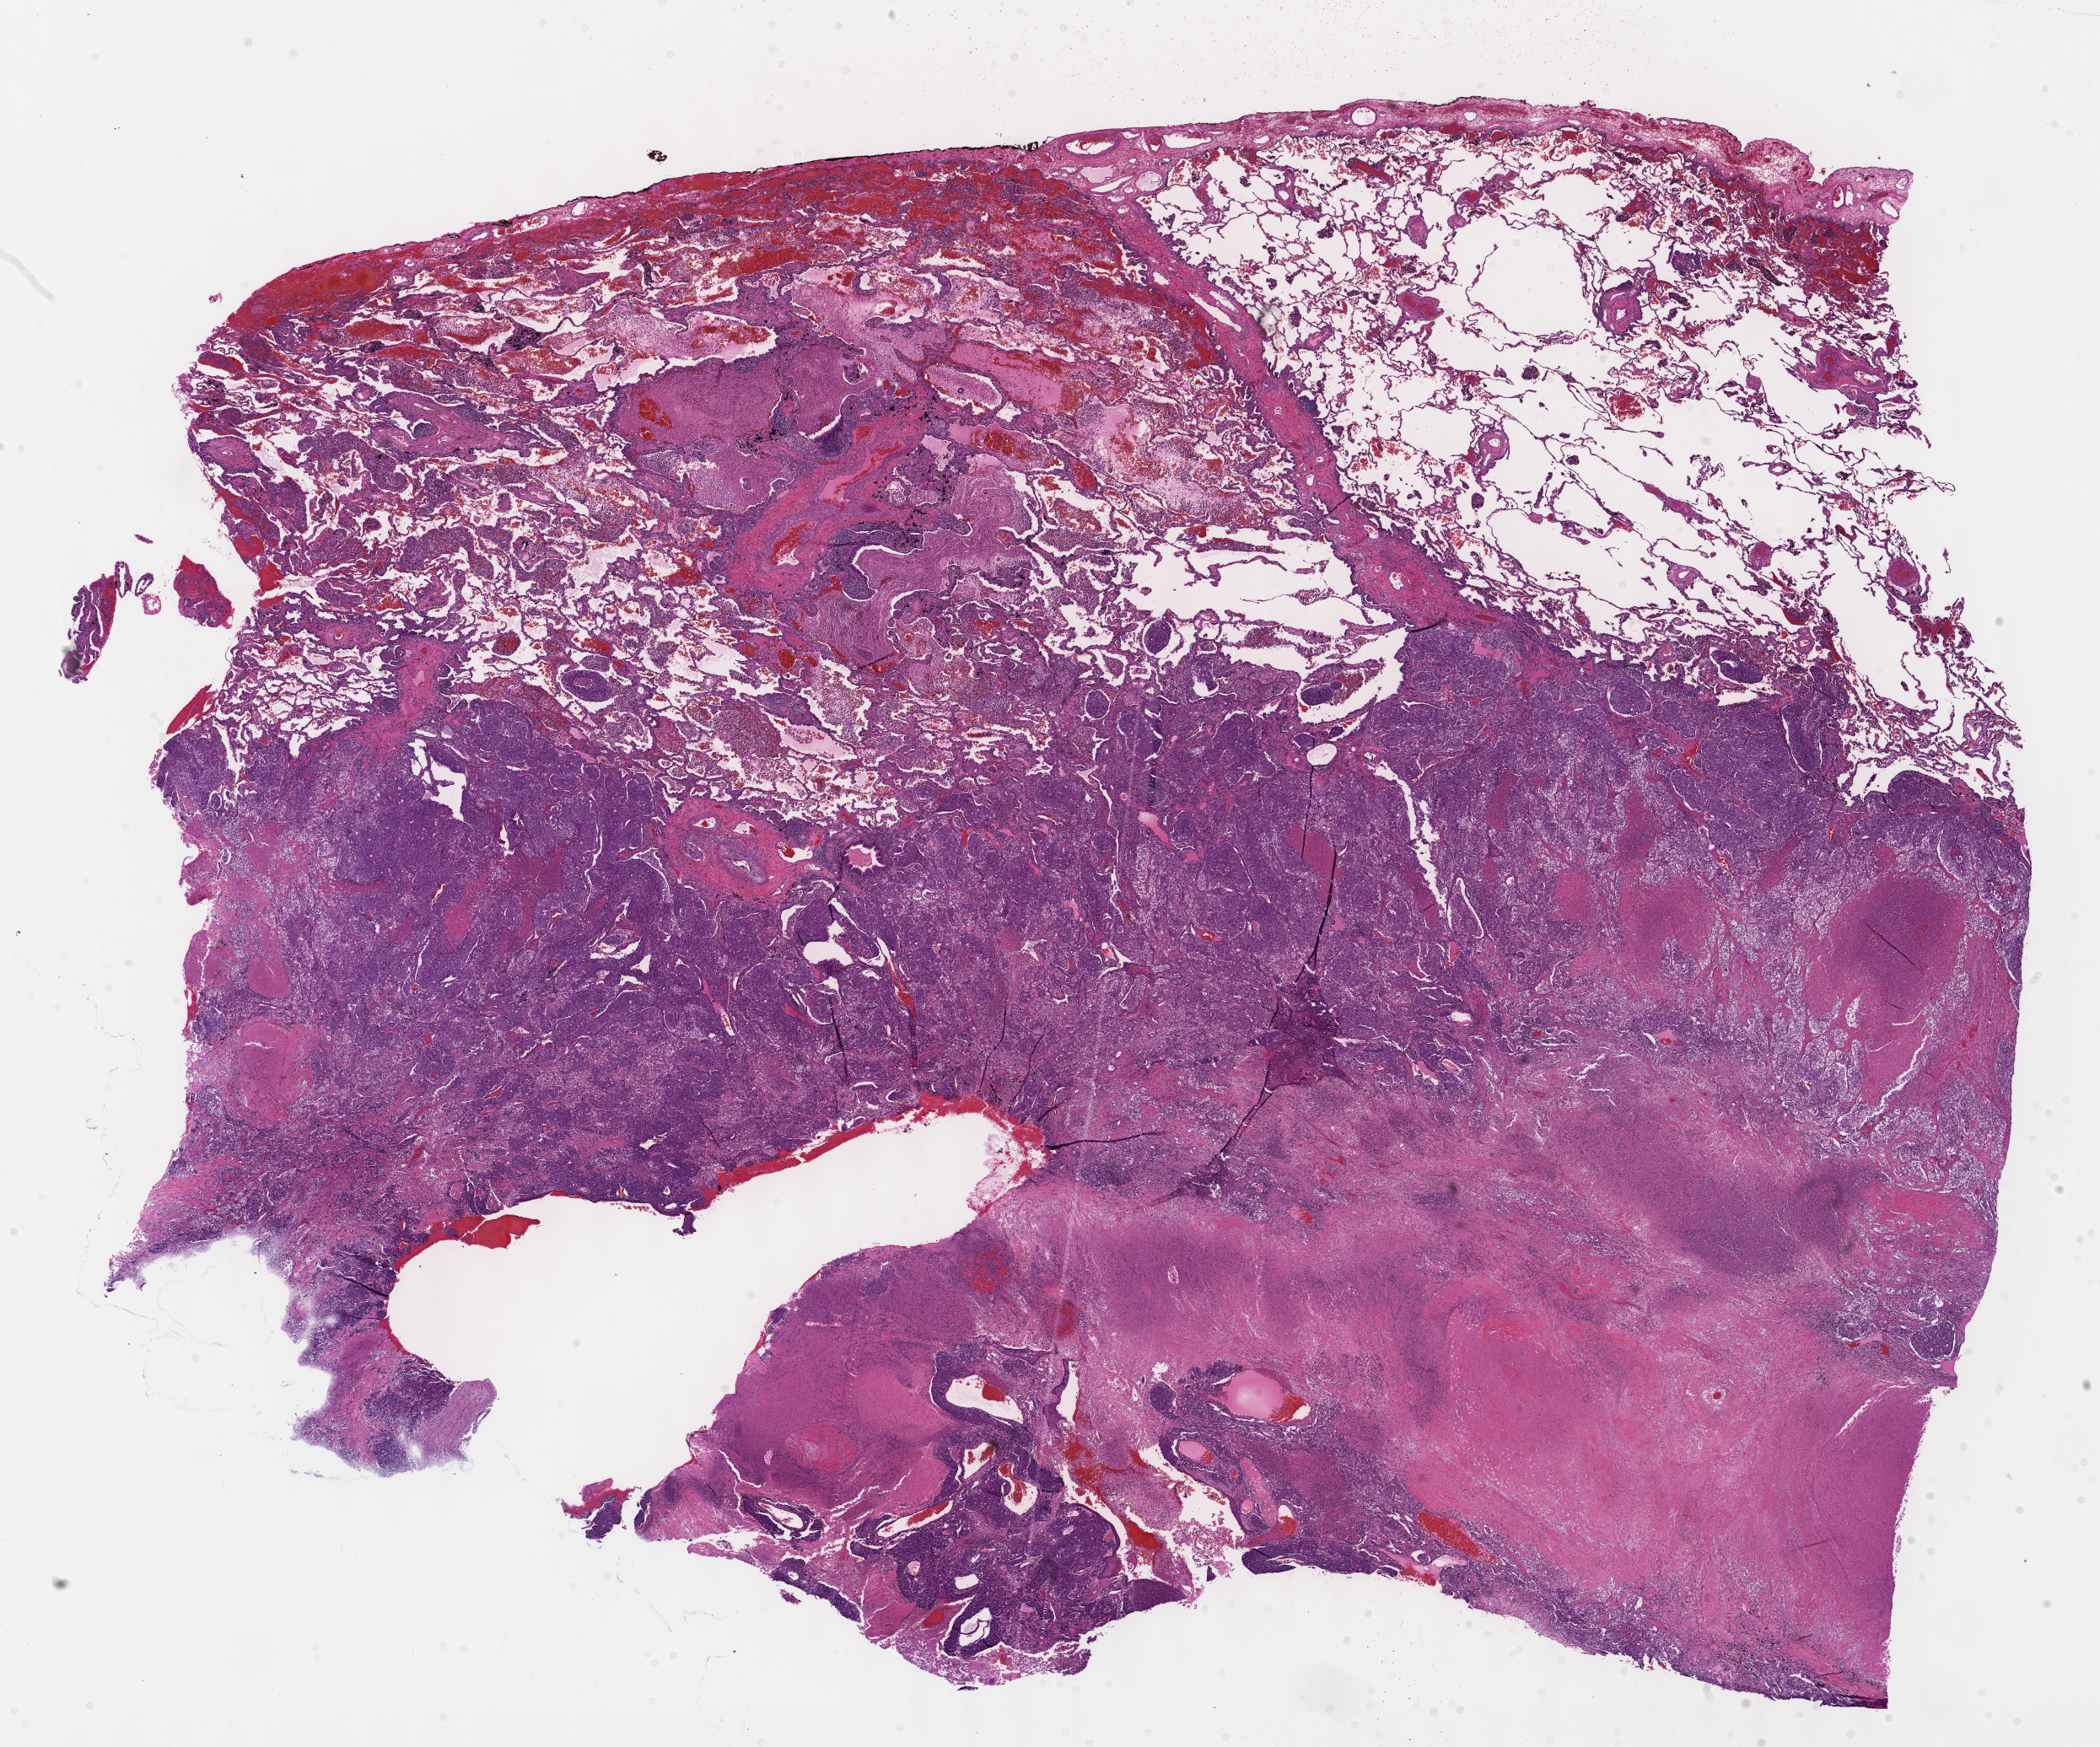
Whole-slide histology image, H&E-stained — low-resolution overview of the scanned area, about 20.1 x 16.7 mm; formalin-fixed paraffin-embedded (FFPE) diagnostic section; lung, primary tumour sample. Male patient; age at initial diagnosis 66 years.
Diagnosis: Squamous cell carcinoma, NOS. AJCC pathologic stage: IB (5th edition).